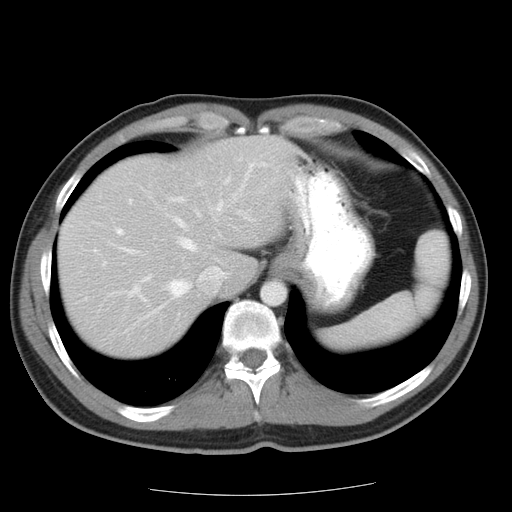
Contrast-enhanced abdominal CT, one axial slice. Slice 17 of 22 in the series (ordered by position). 120 kVp. Intravenous contrast given. Soft-tissue window (W 400 / L 40 HU). 7.5 mm slice thickness. 512 × 512 image matrix, field of view 359 × 359 mm. Male patient, age 41 years. Case-level facts recorded for this patient, not image findings: diagnosis: colorectal cancer liver metastases, imaged before liver resection; multiple liver metastases: no; largest metastasis: 2.7 cm.
Structures marked on this image (outlined manually by an expert reader):
- hepatic veins: bounding box (x1, y1, x2, y2) in pixels: (126, 203, 223, 297)
- liver: (60, 137, 291, 355)
- planned liver remnant (the part of the liver to remain after resection): (60, 137, 292, 330)
- portal vein (with intrahepatic branches): (118, 165, 252, 296)